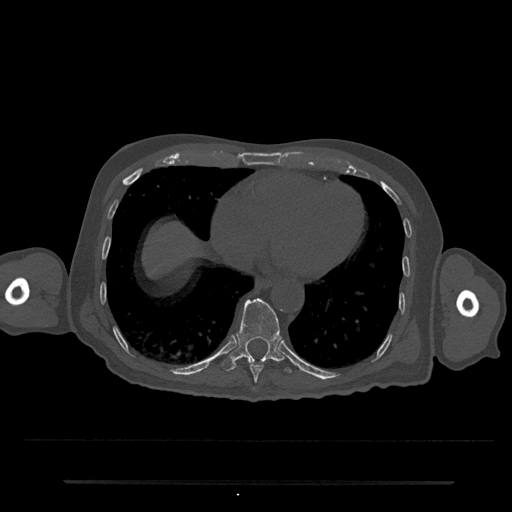
CT including the spine, one axial slice; slice 332 of 797 in the series (ordered by position); reconstruction kernel Br40s/3; 120 kVp; bone window (W 1800 / L 400 HU); 0.5 mm slice thickness; 512 × 512 image matrix, field of view 427 × 427 mm. Male patient, age 74 years. Case-level facts recorded for this patient, not image findings: primary cancer: prostate.
Outlined on this slice (semi-automatic segmentation, software-assisted and operator-edited):
- T10 vertebra: box from (x=222, y=298) to (x=292, y=374) px
- T9 vertebra: (x=250, y=361)–(x=264, y=390)